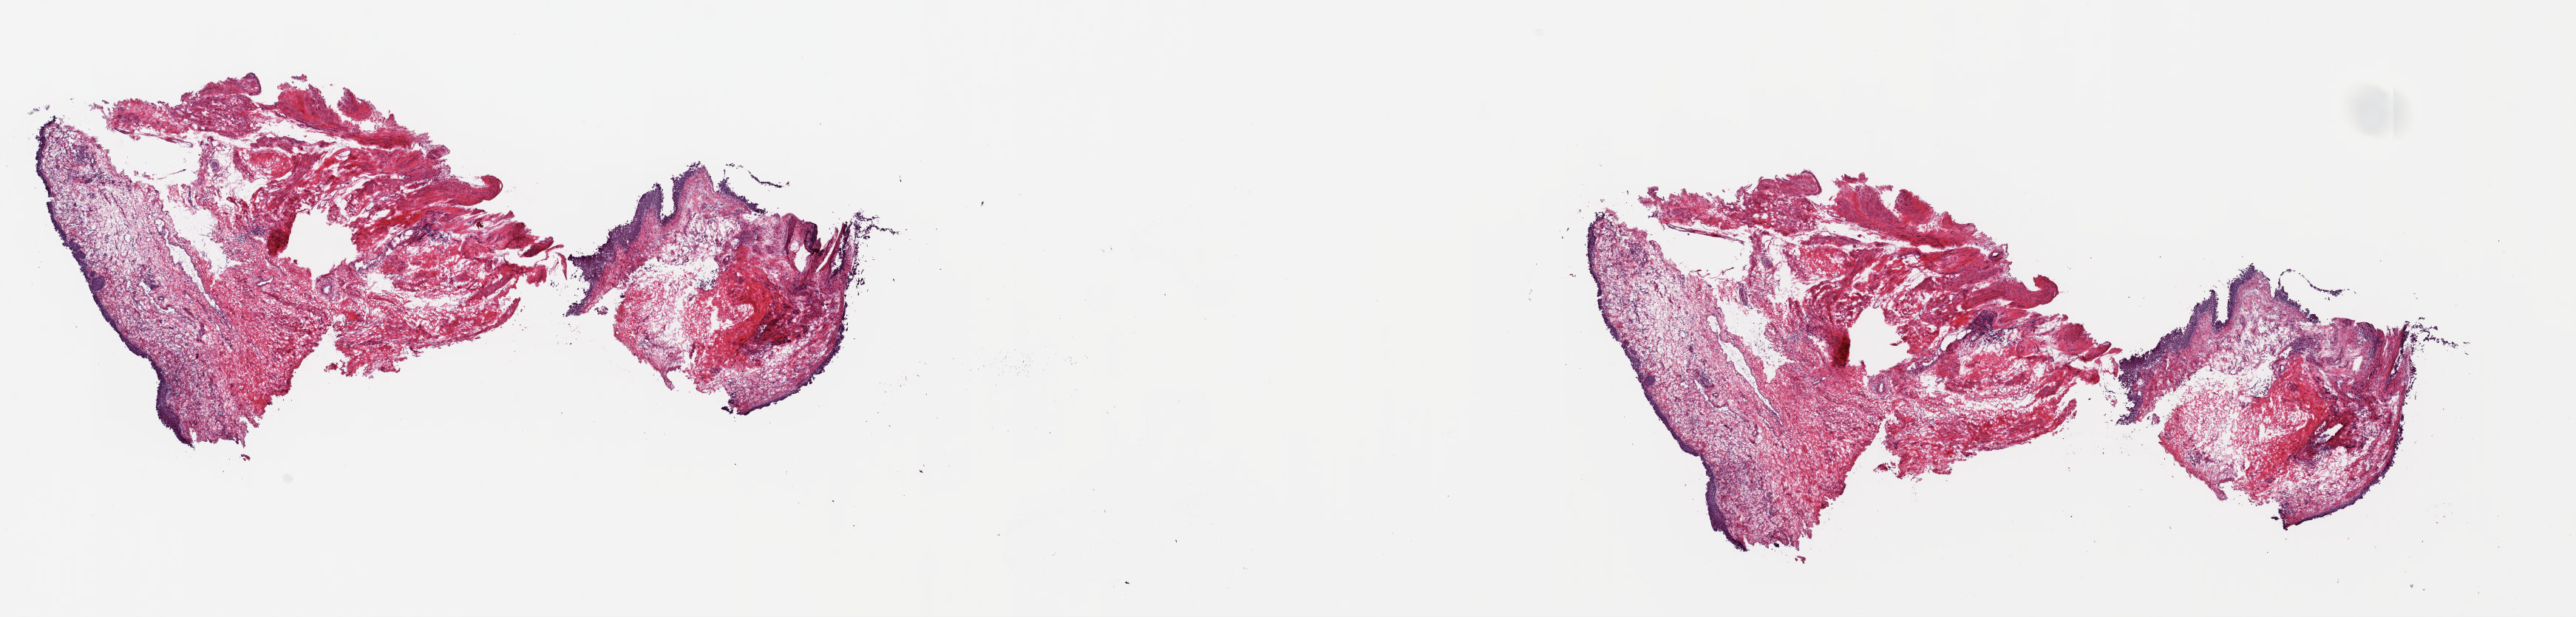
Digitized H&E-stained tissue section (whole slide) — whole scanned area (about 27.5 x 6.6 mm, from a 20x scan) shown as a low-resolution overview; frozen section; bladder, solid tissue normal (non-tumour tissue) sample. Female patient; age at initial diagnosis 84 years. Slide review estimates, as recorded: tumour cells 0%, tumour nuclei 0%, normal cells 10%, stromal cells 90%, necrosis 0%. Infiltration values recorded for this section: lymphocyte infiltration 0%, monocyte infiltration 0%, neutrophil infiltration 0%.
- this section: solid tissue normal (non-tumour) sample from the same patient
- patient diagnosis: Transitional cell carcinoma